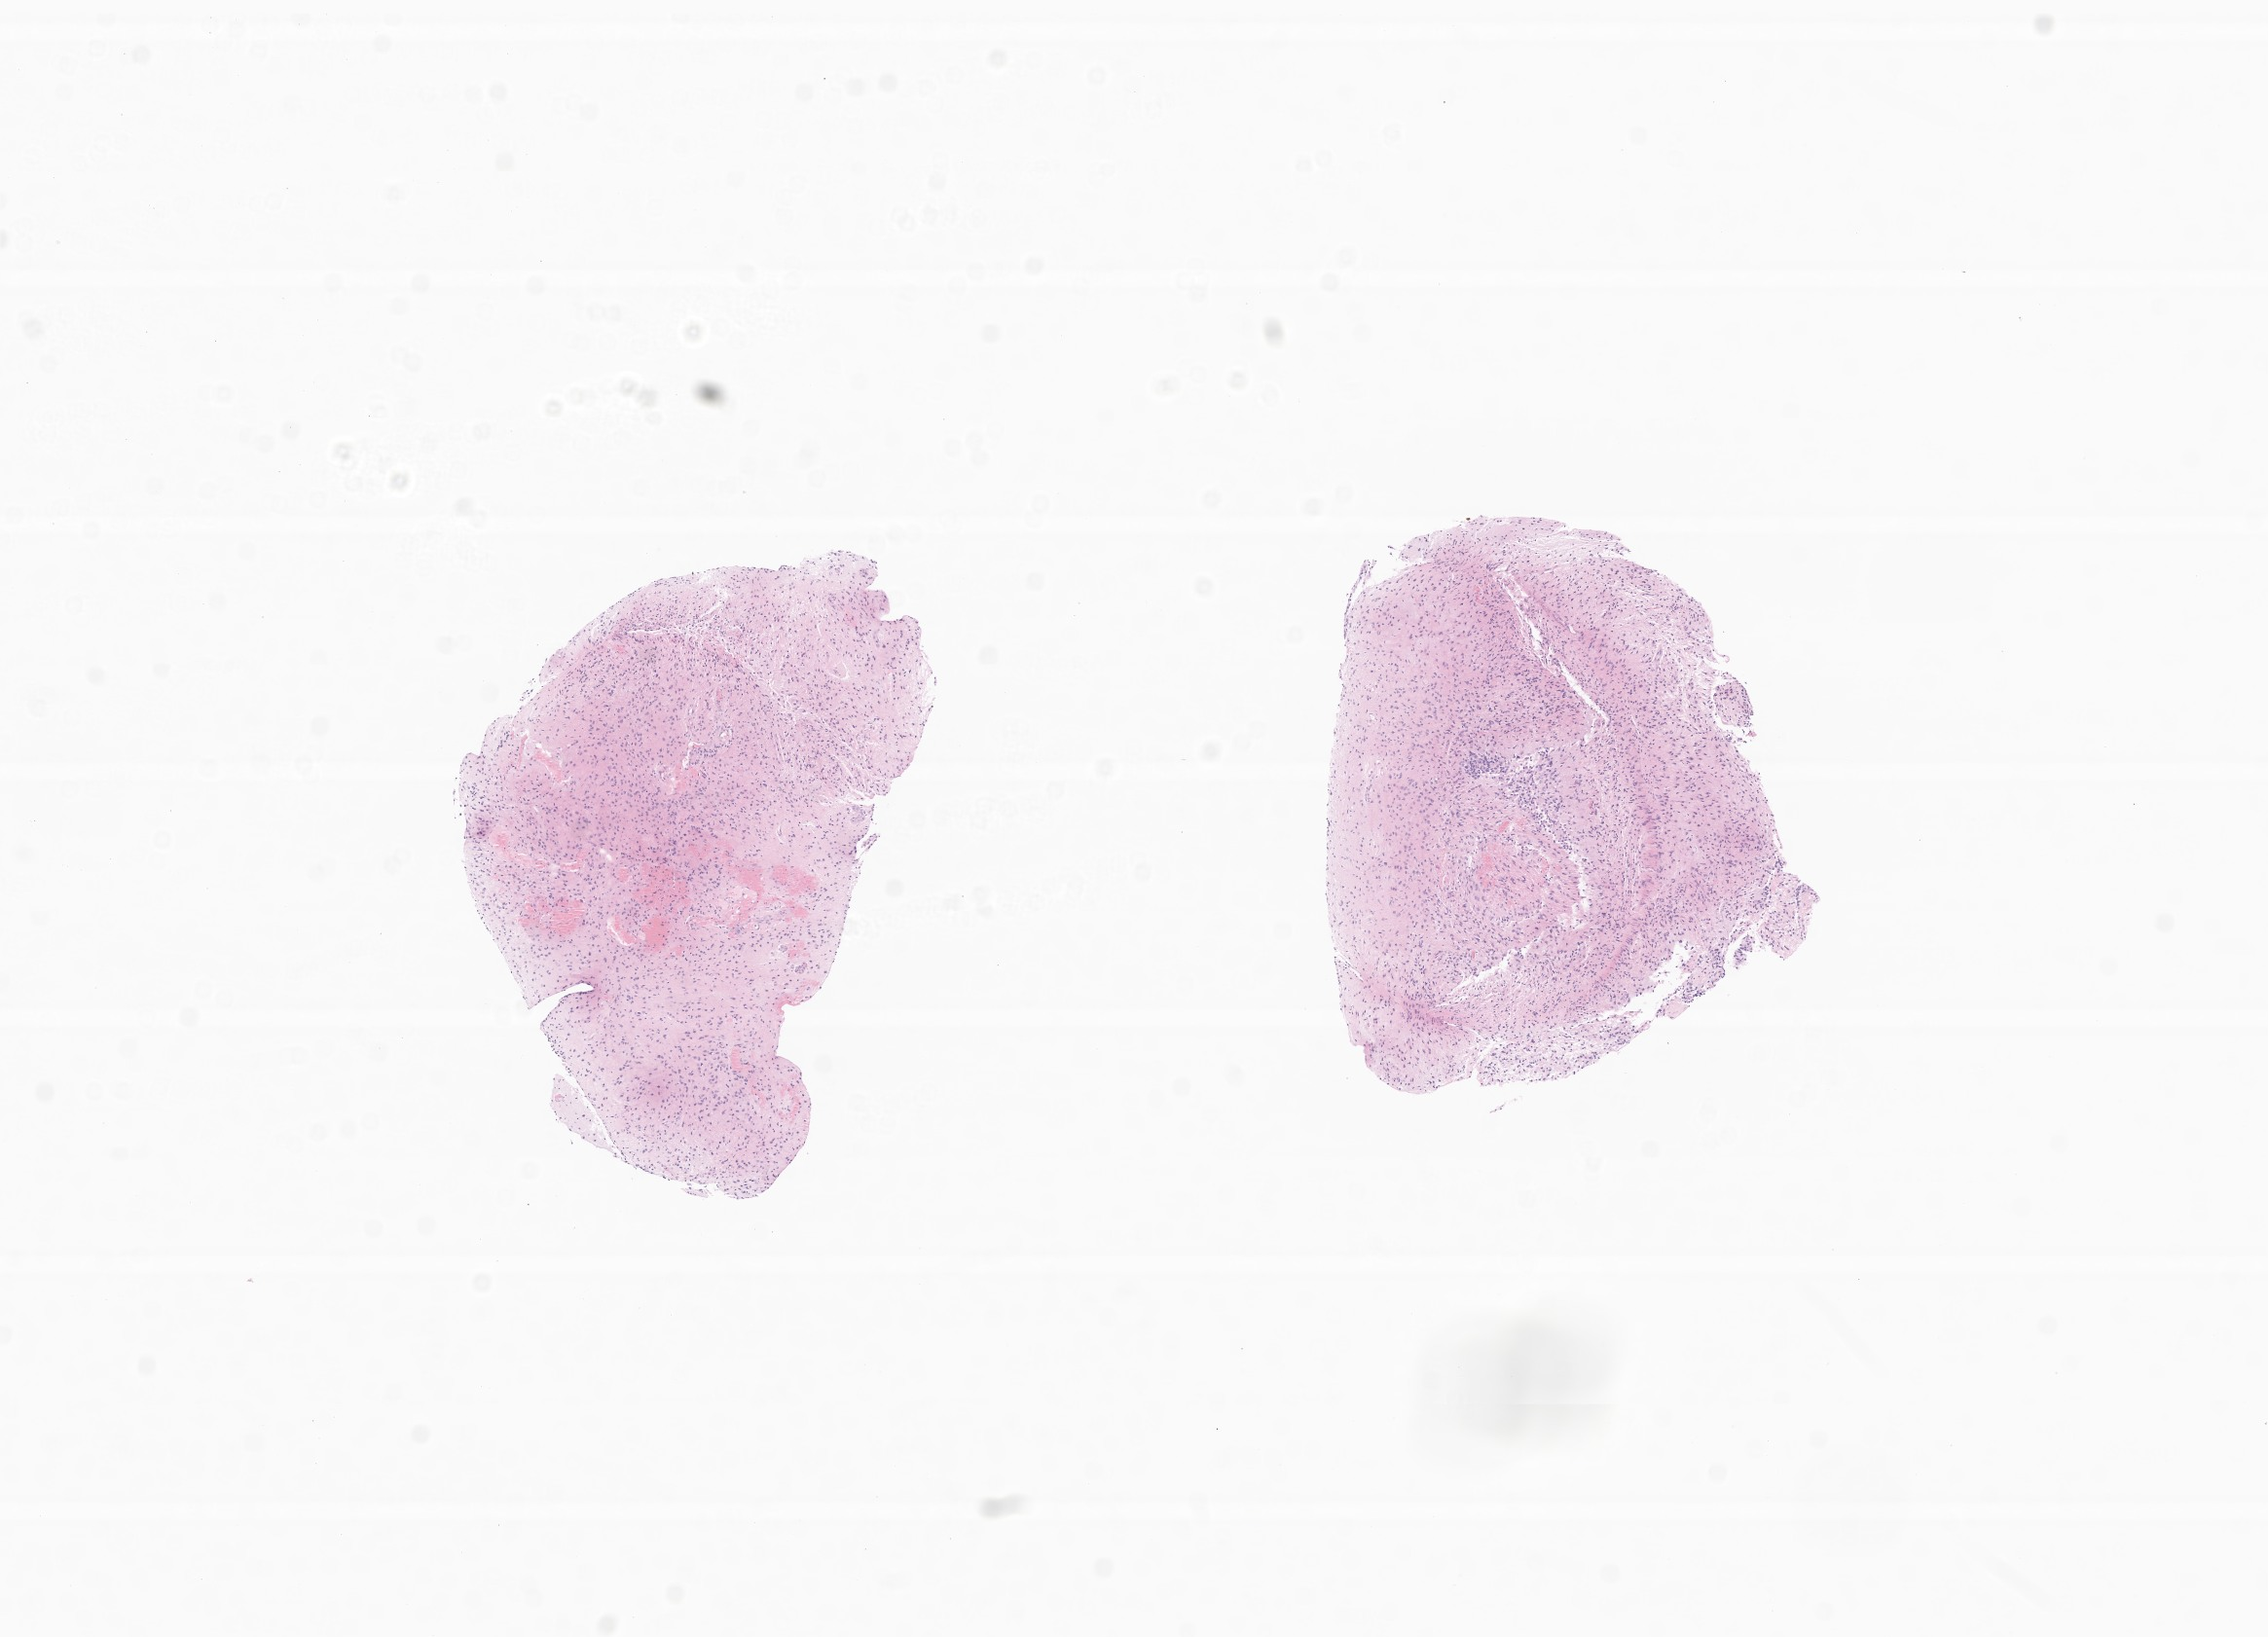
Whole-slide image, H&E stain of tumor tissue from the pineal gland — shown as a low-resolution overview of the whole scanned area (about 9.8 x 7.1 mm). Formalin-fixed, paraffin-embedded (FFPE) tissue. Patient male; age 130 months.
Recorded diagnosis: Oligoastrocytoma, NOS.